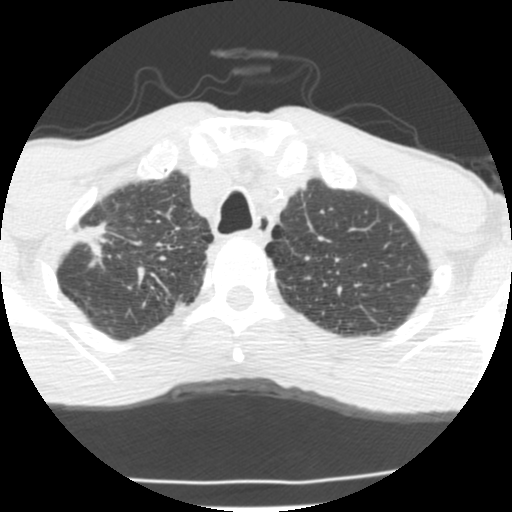
Chest CT (low-dose screening protocol), one axial image, second screening round (one year after baseline), lung window (W 1500 / L -600 HU), standard (soft-tissue) reconstruction kernel (STANDARD), 120 kVp. Male participant, aged 62 years at enrolment. Current smoker at enrolment.
Lesion marked by an expert reader, bounding box (x1, y1, x2, y2) in pixels: (56, 215, 132, 271). The exam's reader record, not a measurement of the box and not confirmed to be the same lesion: non-calcified nodule or mass ≥4 mm, right upper lobe, 23 × 11 mm, spiculated (stellate) margins, soft tissue attenuation, pre-existing on the prior screen: yes. Official screen result: positive, change unspecified: nodule(s) >= 4 mm or enlarging nodule(s), mass(es), or other non-specific abnormalities suspicious for lung cancer. Later outcome: lung cancer diagnosed 277 days after this screen — adenocarcinoma, NOS, right upper lobe, poorly differentiated (G3), stage IIA (AJCC 6th edition), 22 mm at pathology.